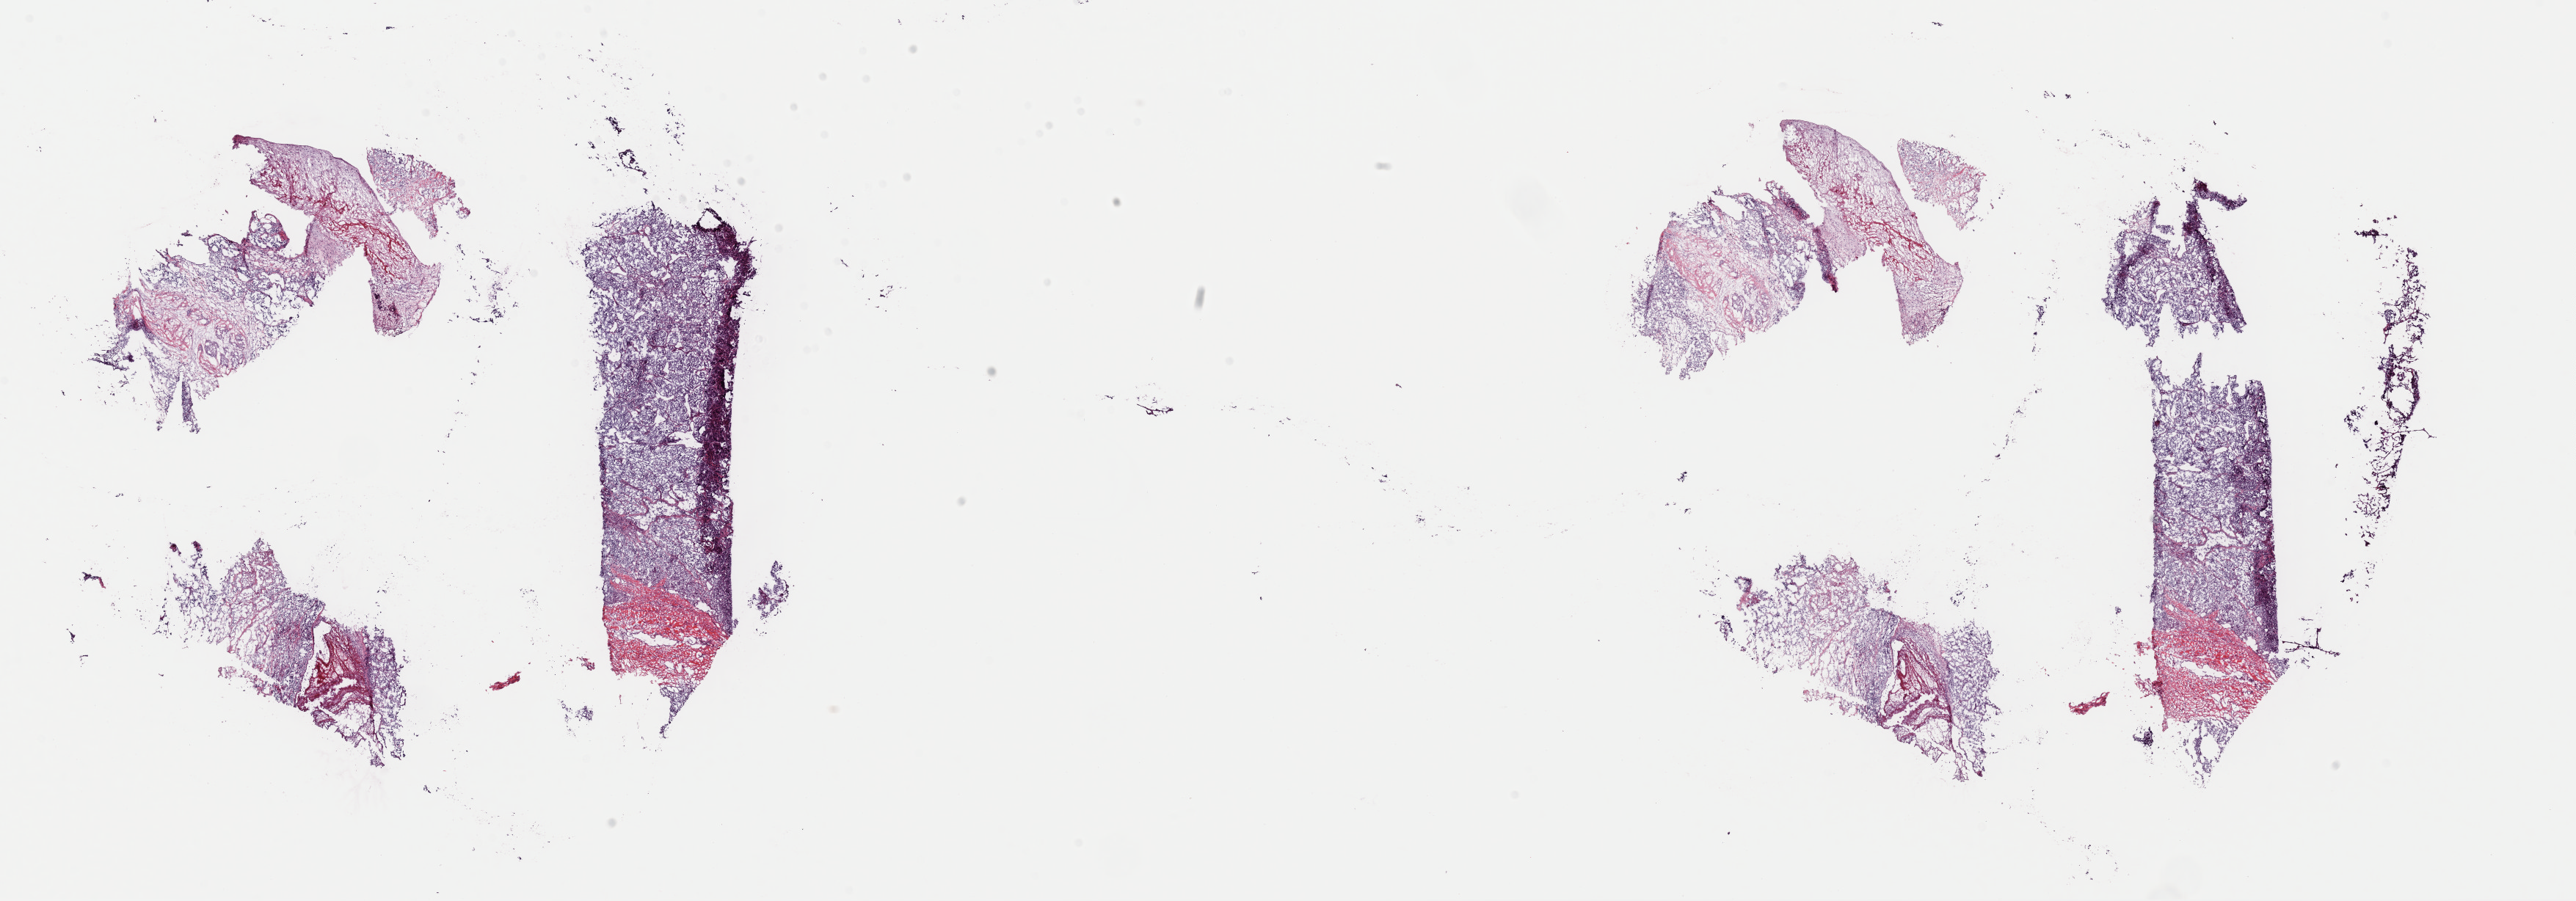
Digitized H&E tissue section (whole slide) — a low-resolution overview of the entire scanned area, about 27.7 x 9.7 mm. Frozen section. Retroperitoneum and peritoneum, primary tumour sample. Patient: female, age at initial diagnosis 63 years.
Histologic diagnosis: Pheochromocytoma, NOS (retroperitoneum).